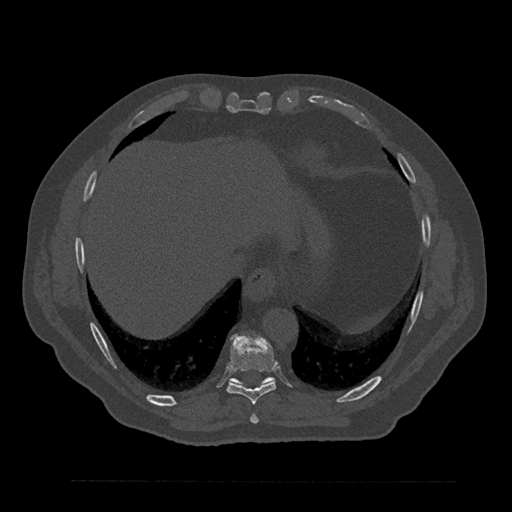
CT including the spine, one axial slice; position 393 of 797 along the scan axis; reconstruction kernel Br40s/3; 120 kVp; bone window (W 1800 / L 400 HU); 0.5 mm slice thickness; 512 × 512 image matrix, field of view 430 × 430 mm. Patient: male, 61 years. From the clinical record (not read from this slice): primary cancer: prostate.
Outlined on this slice (semi-automatically segmented with operator editing):
- T10 vertebra: box from (x=230, y=377) to (x=274, y=386) px
- T8 vertebra: (x=250, y=414)–(x=259, y=424)
- T9 vertebra: (x=227, y=334)–(x=278, y=405)